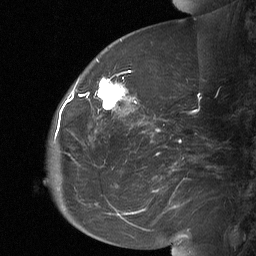
Breast MRI (dynamic contrast-enhanced), one sagittal slice; position 23 of 64 along the scan axis; dynamic contrast-enhanced study with each time point stored as its own series, time point 2 of 3 at this slice position (early post-contrast, ordered by acquisition time); 1.5 T; TE 4.8 ms, TR 27 ms; 2 mm slice thickness; 256 × 256 image matrix, field of view 200 × 200 mm. Female patient, age 60 years. Case-level facts recorded for this patient, not image findings: setting: breast cancer imaged before/during neoadjuvant chemotherapy; receptor status: HR-positive, HER2-negative.
Structures marked on this image (semi-automatically segmented with operator editing):
- analysis volume of interest (the breast-tissue region the enhancement analysis was run in; not a lesion): bounding box [x1, y1, x2, y2] px = [92, 70, 134, 112]
- tumour enhancement mask (voxels above the 90 % enhancement threshold inside the analysis volume of interest): [98, 71, 130, 110]